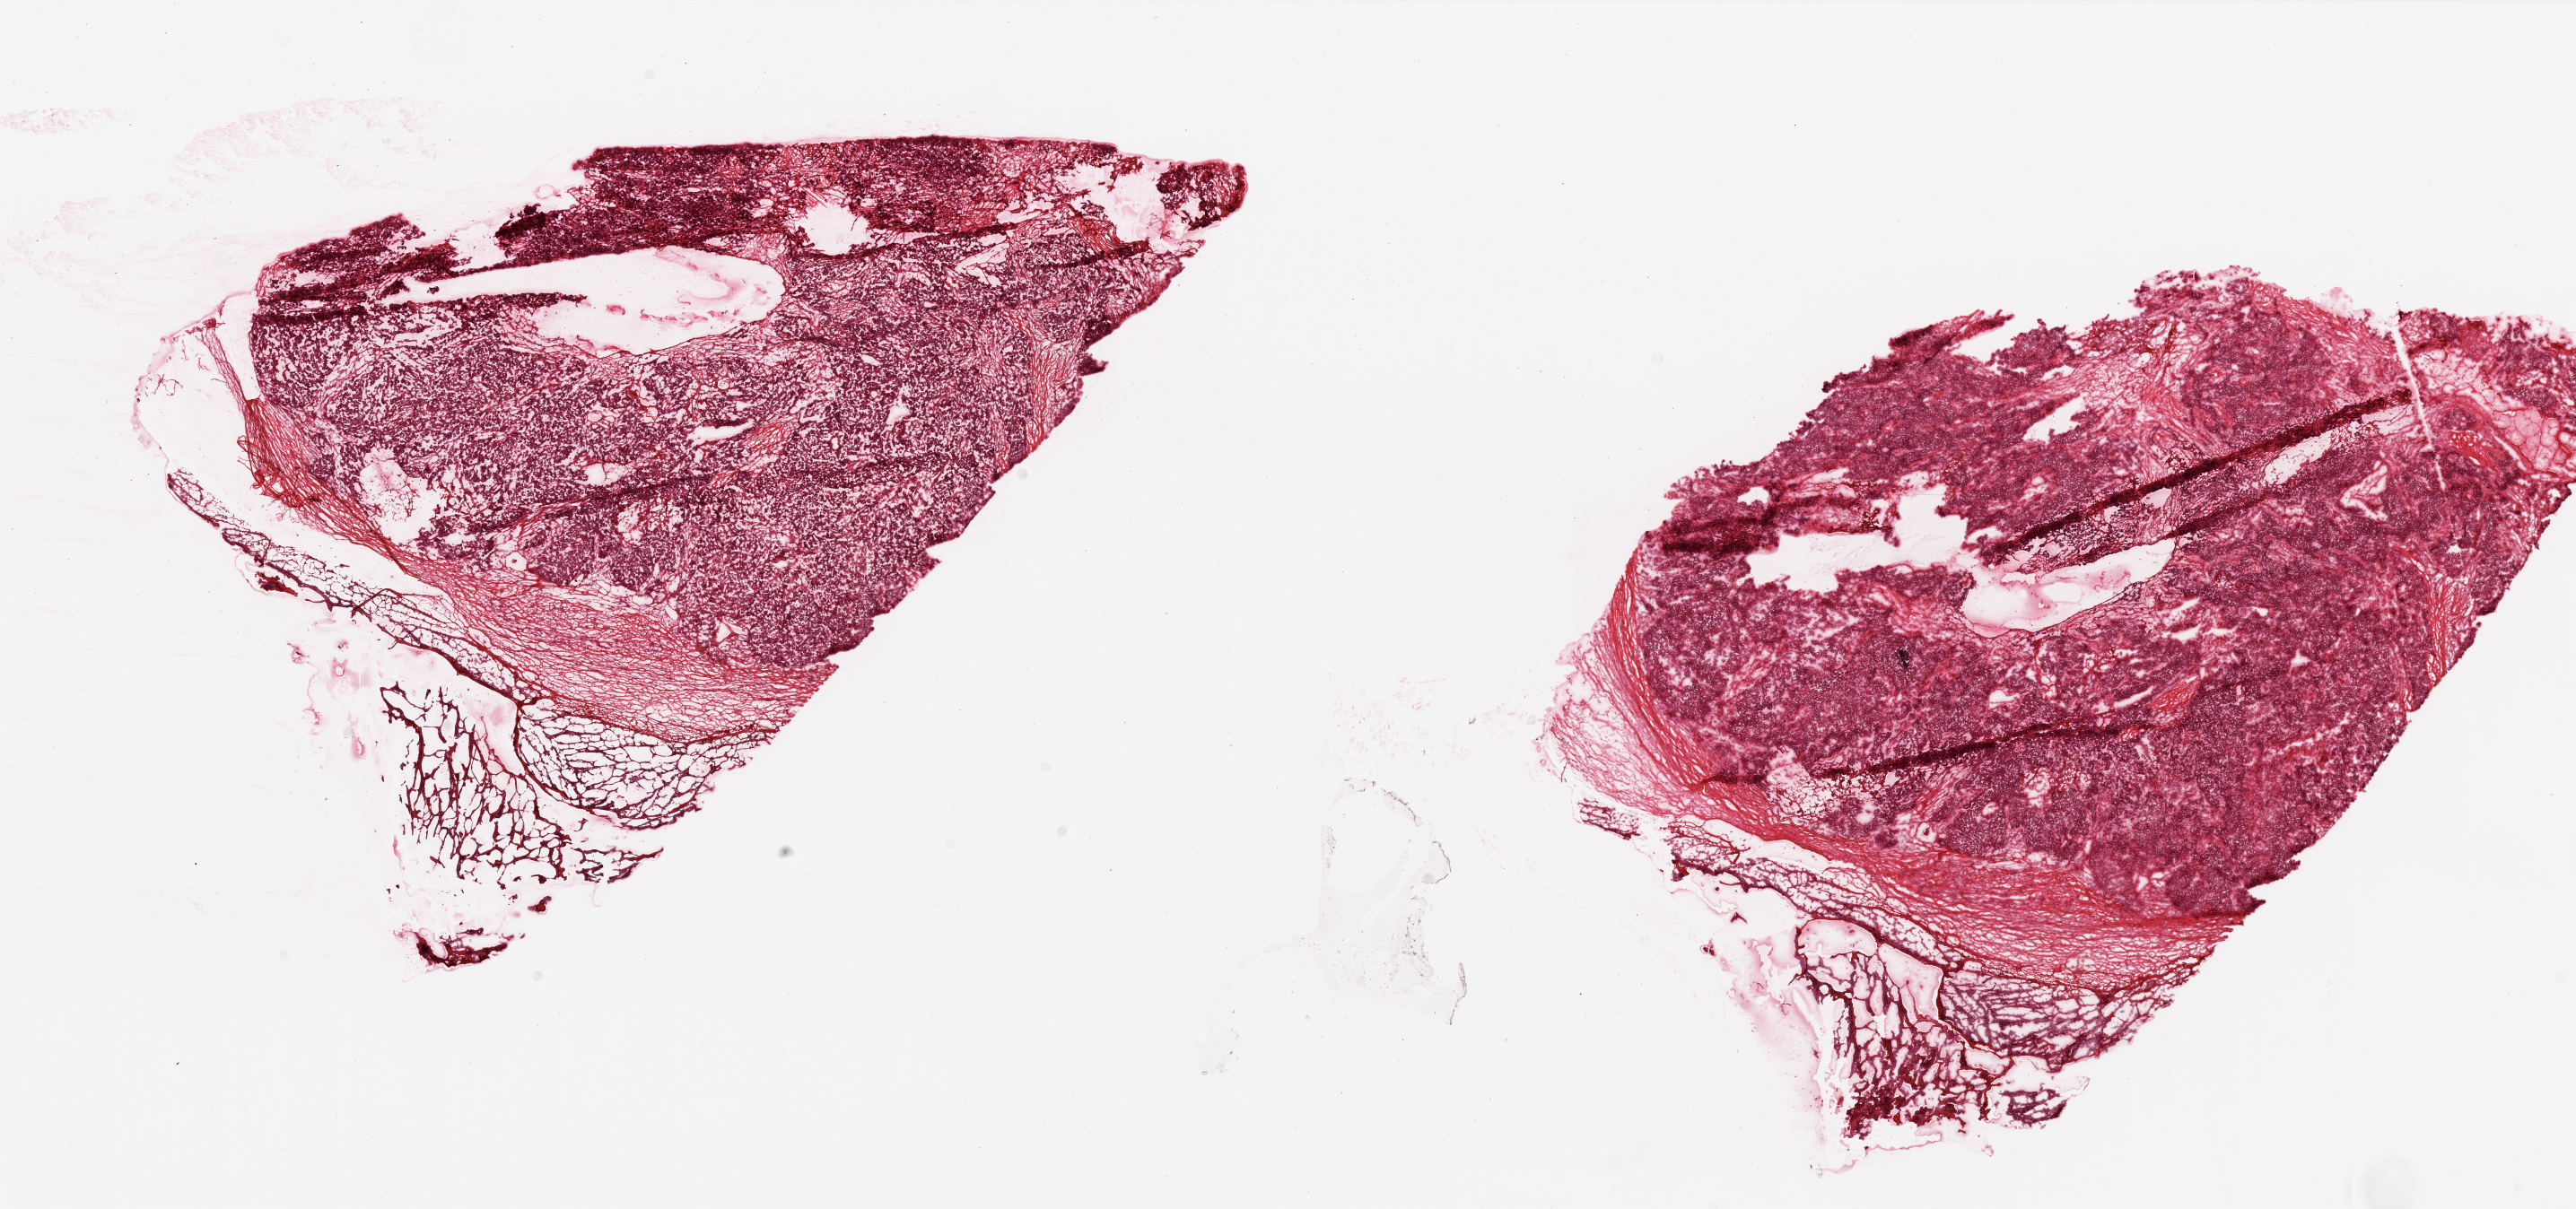
Digitized Hematoxylin and eosin (H&E) stained tissue section (whole slide) — shown as a low-resolution overview of the whole scanned area (about 23.0 x 10.8 mm, from a 20x scan), frozen section, sample: primary tumour, ovary. Female patient; age at initial diagnosis 53 years. Histologic grade: G3 (poorly differentiated). Composition of this section per pathologist review: tumour cells 70%, tumour nuclei 90%, normal cells 0%, stromal cells 30%, necrosis 0%.
- laterality: bilateral
- FIGO stage: IIIC
- pathologic diagnosis: Serous cystadenocarcinoma, NOS